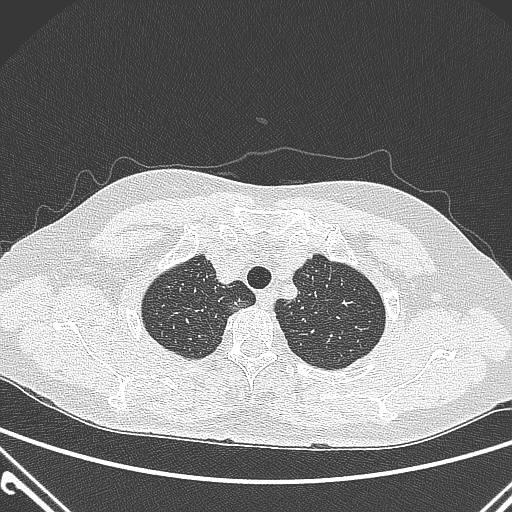
Chest CT, one axial slice; slice 245 of 300 in the series (ordered by position); 120 kVp; lung window (W 1500 / L -600 HU); 512 × 512 image matrix, field of view 350 × 350 mm. Patient: female, 54 years. From the clinical record (not read from this slice): clinical TNM (as recorded): T1a N0 M0.
Outlined on this slice (rectangle marked by the reading radiologist):
- lung tumour (recorded histology: adenocarcinoma): box from (x=224, y=295) to (x=251, y=317) px